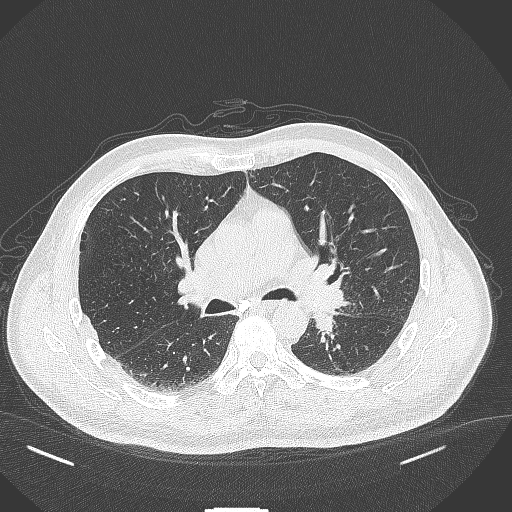
Chest CT, one axial slice; position 247 of 429 along the scan axis; reconstruction kernel B70f; lung window (W 1500 / L -600 HU); 512 × 512 image matrix. Male patient, age 55 years. Case-level facts recorded for this patient, not image findings: clinical TNM (as recorded): T3 N0 M1c.
Structures marked on this image (rectangle marked by the reading radiologist):
- lung tumour (recorded histology: adenocarcinoma): bounding box [x1, y1, x2, y2] px = [310, 305, 337, 339]